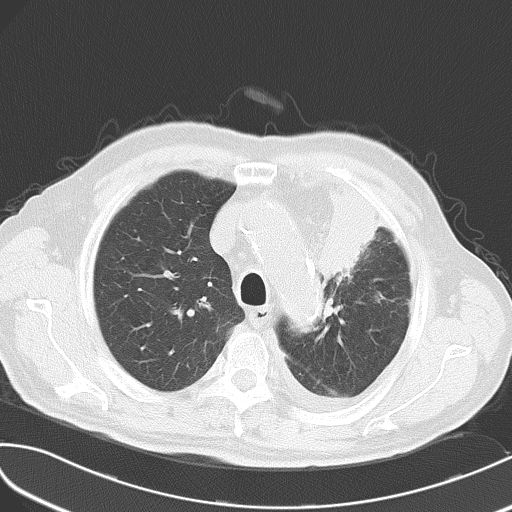
Chest CT, one axial slice. Position 42 of 54 along the scan axis. Reconstruction kernel B70f. Lung window (W 1500 / L -600 HU). 5 mm slice thickness. 512 × 512 image matrix, field of view 353 × 353 mm. Male patient, age 70 years. Case-level facts recorded for this patient, not image findings: clinical TNM (as recorded): T2 N1 M3; histopathological grade: G3.
Structures marked on this image (bounding box drawn by a radiologist):
- lung tumour (recorded histology: small cell carcinoma): bounding box (x1, y1, x2, y2) in pixels: (319, 174, 389, 291)